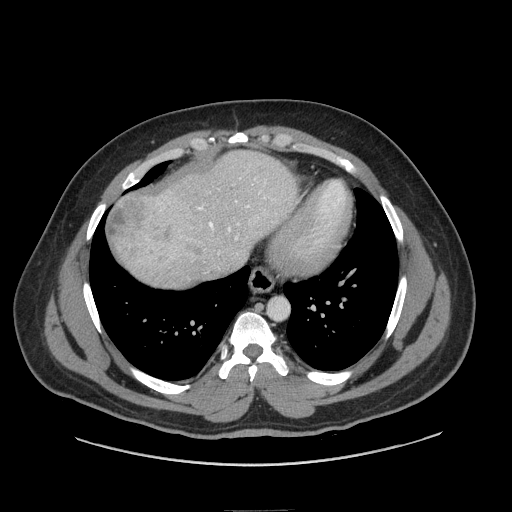
Contrast-enhanced abdominal CT (liver protocol), one axial slice; slice 71 of 87 in the series (ordered by position); reconstruction kernel STANDARD; 140 kVp; soft-tissue window (W 400 / L 40 HU); 512 × 512 image matrix, field of view 440 × 440 mm. Case-level facts recorded for this patient, not image findings: diagnosis: hepatocellular carcinoma (patient treated with transarterial chemoembolisation; whether this scan precedes or follows treatment is not stated here); TNM stage (as recorded): Stage-II; Child-Pugh class: A; tumour differentiation: moderately differentiated; tumour nodularity: uninodular.
Outlined on this slice (semi-automatically segmented with operator editing):
- abdominal aorta: bounding box [x1, y1, x2, y2] px = [268, 298, 288, 319]
- liver parenchyma outside the tumour (the mass and vessels are separate outlines, so this box may not span the whole liver): [112, 150, 296, 288]
- mass: [107, 194, 185, 264]
- liver vessels: [198, 205, 249, 239]